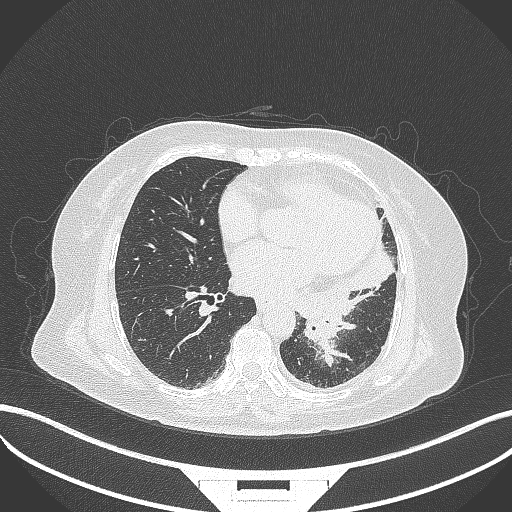
Chest CT, one axial slice. Position 152 of 322 along the scan axis. Reconstruction kernel B70f. 120 kVp. Lung window (W 1500 / L -600 HU). 1 mm slice thickness. 512 × 512 image matrix, field of view 400 × 400 mm. Female patient, age 69 years. From the clinical record (not read from this slice): clinical TNM (as recorded): T2b N3 M1.
Annotated regions visible in this slice (bounding box drawn by a radiologist):
- lung tumour (recorded histology: adenocarcinoma): bounding box [x1, y1, x2, y2] px = [301, 304, 349, 352]